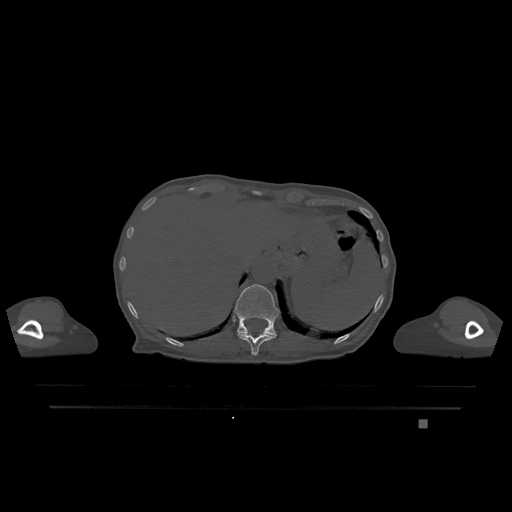
CT including the spine, one axial slice; position 560 of 1317 along the scan axis; bone window (W 1800 / L 400 HU); 0.5 mm slice thickness; 512 × 512 image matrix, field of view 500 × 500 mm. Female patient, age 74 years. Case-level facts recorded for this patient, not image findings: primary cancer: lung; vertebrae with lytic lesions (as recorded): T1, T4, T5, T6, L4, L5.
Outlined on this slice (semi-automatic segmentation, software-assisted and operator-edited):
- T11 vertebra: bounding box <238,328,276,355> (left, top, right, bottom; pixels)
- T12 vertebra: <234,284,279,336>